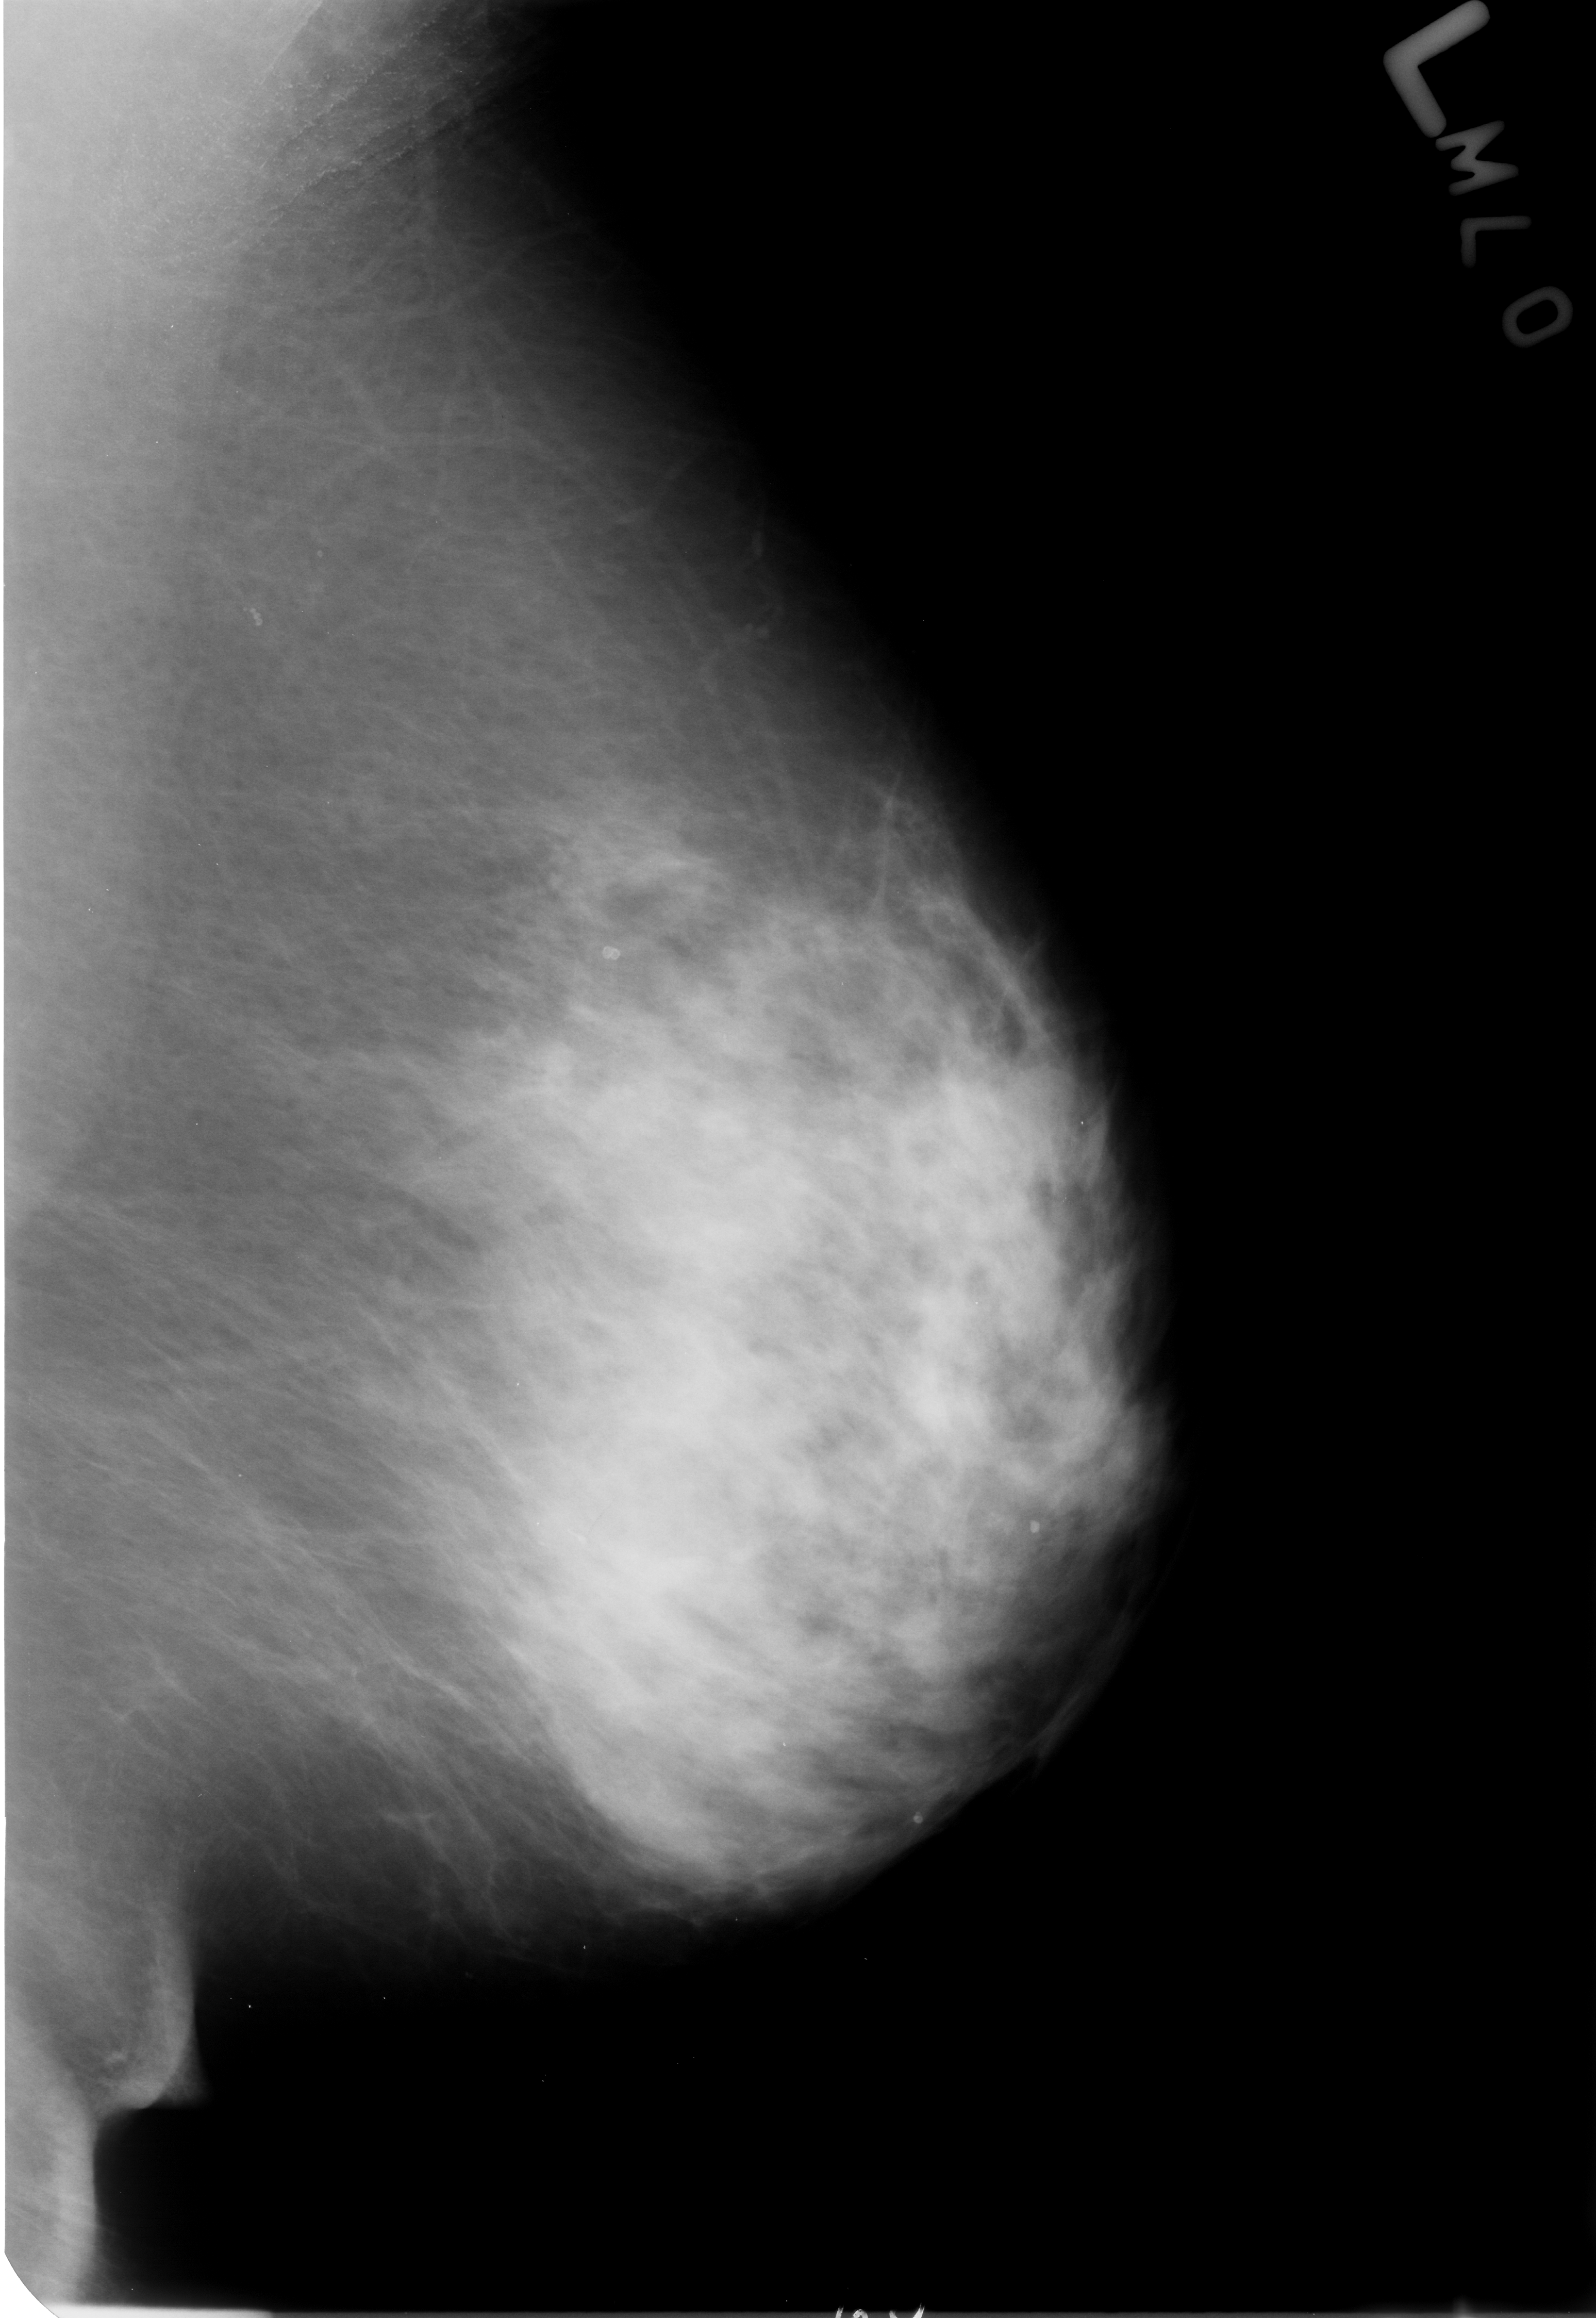
Scanned film-screen mammogram; left breast; MLO view; BI-RADS breast density category 3 (scale 1–4).
- Abnormality record for this image: Finding 1 of 4: calcifications, morphology round and regular / lucent centered; BI-RADS assessment category 2; benign; no additional work-up was recommended (benign without callback).
- Finding 2 of 4: calcifications, morphology round and regular / lucent centered; BI-RADS assessment category 2; benign; no additional work-up was recommended (benign without callback).
- Finding 3 of 4: calcifications, morphology round and regular / lucent centered; BI-RADS assessment category 2; subtlety rating 3 on a 1 (subtle) to 5 (obvious) scale; benign without callback (not worked up further).
- Finding 4 of 4: calcifications, morphology round and regular / lucent centered; BI-RADS assessment category 2; subtlety rating 3 on a 1 (subtle) to 5 (obvious) scale; benign without callback (not worked up further).